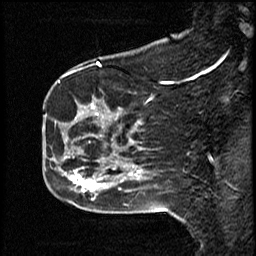
Breast MRI (dynamic contrast-enhanced), one sagittal slice. Position 16 of 50 along the scan axis. Dynamic contrast-enhanced study with each time point stored as its own series, time point 2 of 4 at this slice position (early post-contrast, ordered by acquisition time). 1.5 T. TE 4.2 ms, TR 18.5 ms. 3 mm slice thickness. 256 × 256 image matrix. Patient: female, 44 years. Case-level facts recorded for this patient, not image findings: setting: breast cancer imaged before/during neoadjuvant chemotherapy; receptor status: HR-positive, HER2-negative.
Outlined on this slice (semi-automatic segmentation, software-assisted and operator-edited):
- analysis volume of interest (the breast-tissue region the enhancement analysis was run in; not a lesion): bounding box [x1, y1, x2, y2] px = [59, 80, 114, 206]
- tumour enhancement mask (voxels above the 100 % enhancement threshold inside the analysis volume of interest): [71, 113, 101, 193]